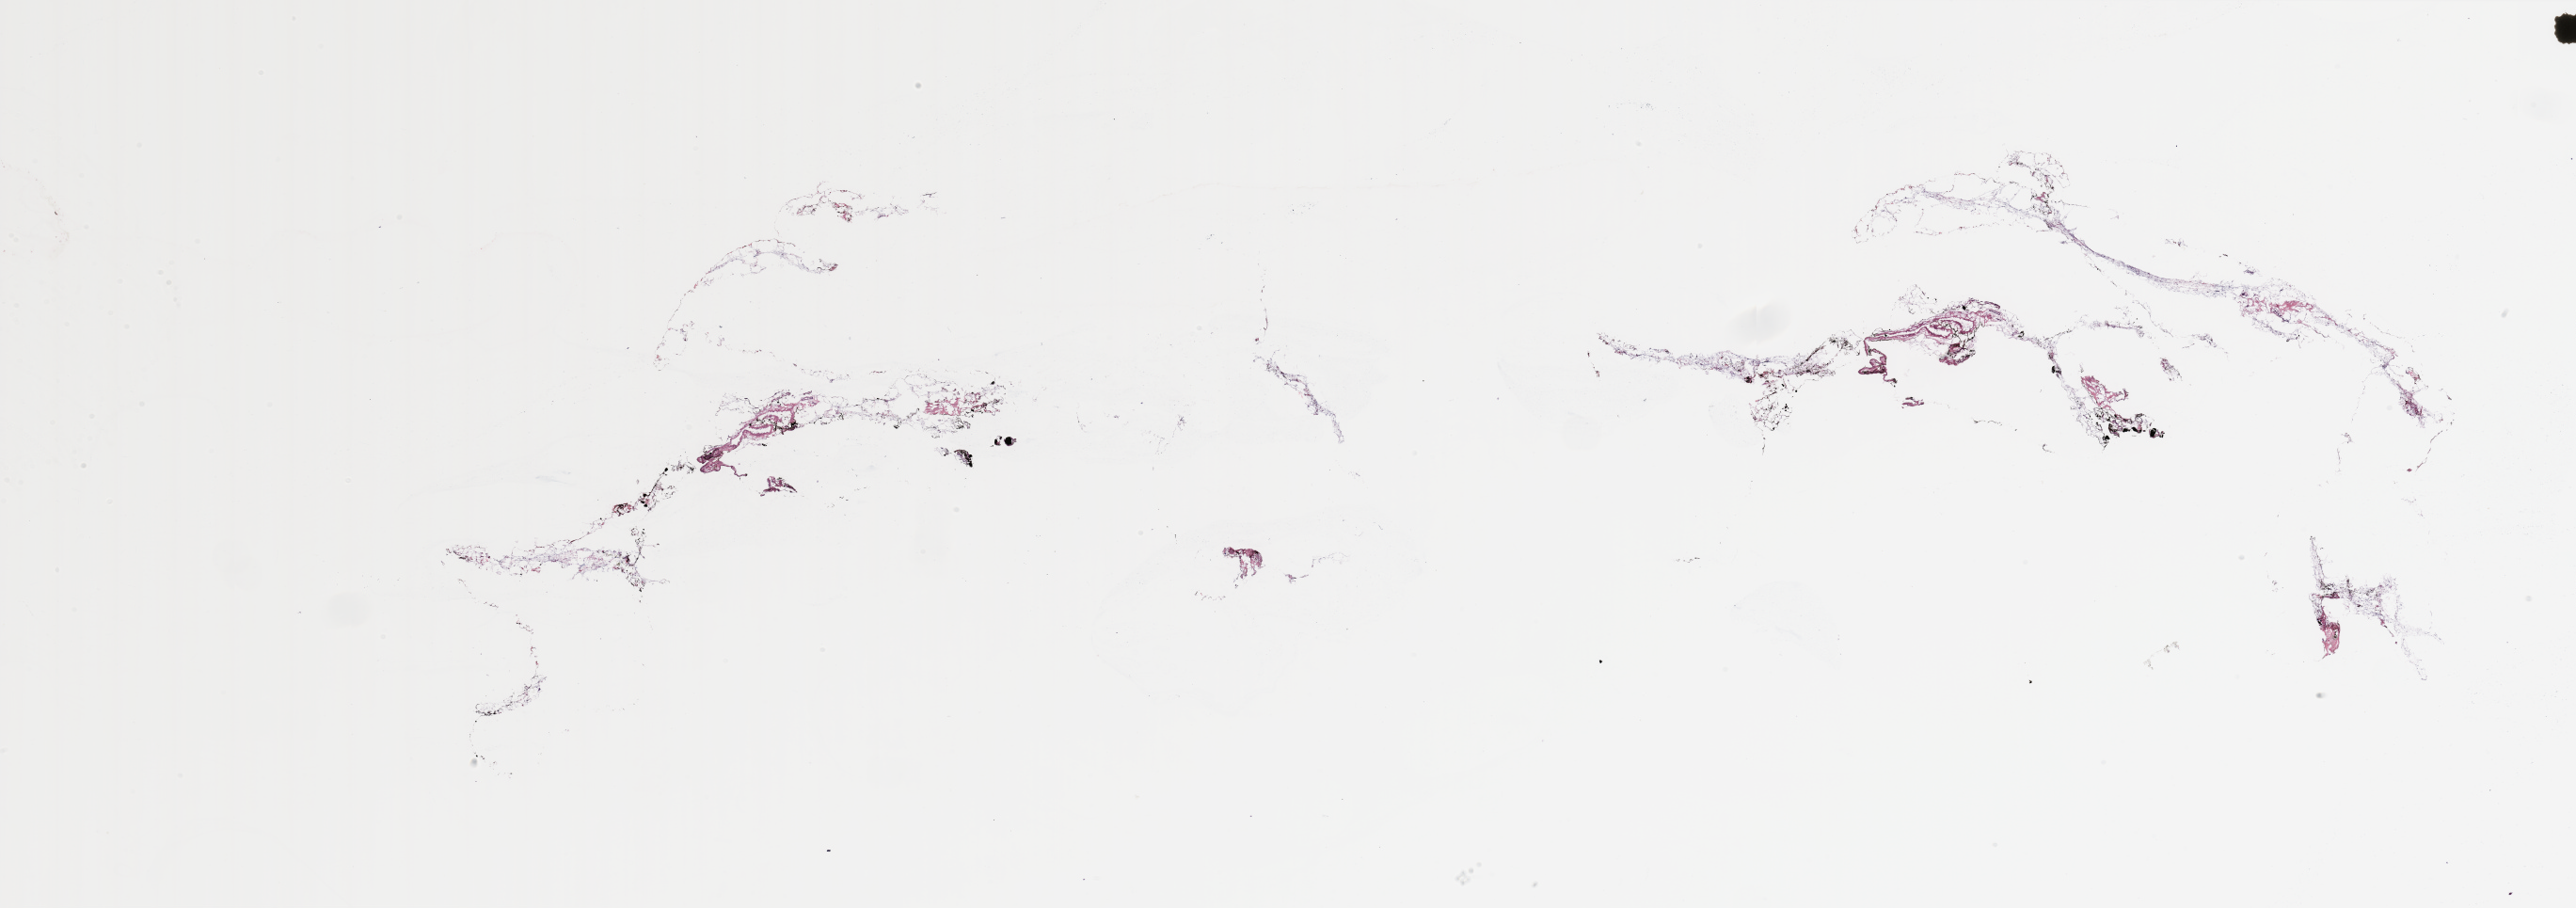
H&E-stained whole-slide image — whole scanned area (about 43.3 x 15.3 mm) shown as a low-resolution overview. Tumour tissue sample, breast. Female, 61 y/o.
AJCC pathologic stage: IIA. Histologic diagnosis: Infiltrating lobular carcinoma, NOS.